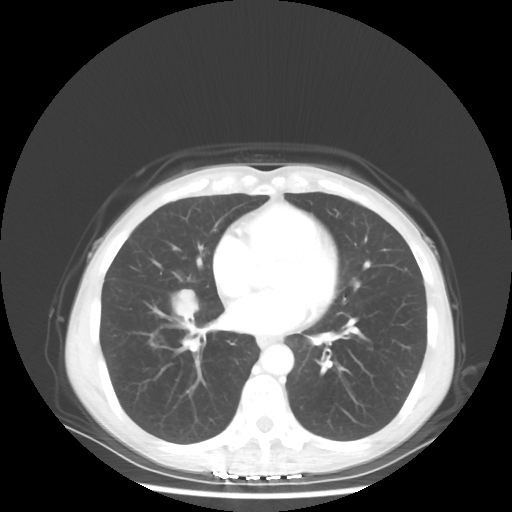
Chest CT, one axial slice. Position 23 of 56 along the scan axis. 80 kVp. Lung window (W 1500 / L -600 HU). 5 mm slice thickness. 512 × 512 image matrix, field of view 360 × 360 mm. Patient: female, 57 years. From the clinical record (not read from this slice): clinical TNM (as recorded): T1c N3 M1a.
Outlined on this slice (bounding box drawn by a radiologist):
- lung tumour (recorded histology: adenocarcinoma): bounding box (x1, y1, x2, y2) in pixels: (171, 284, 204, 323)